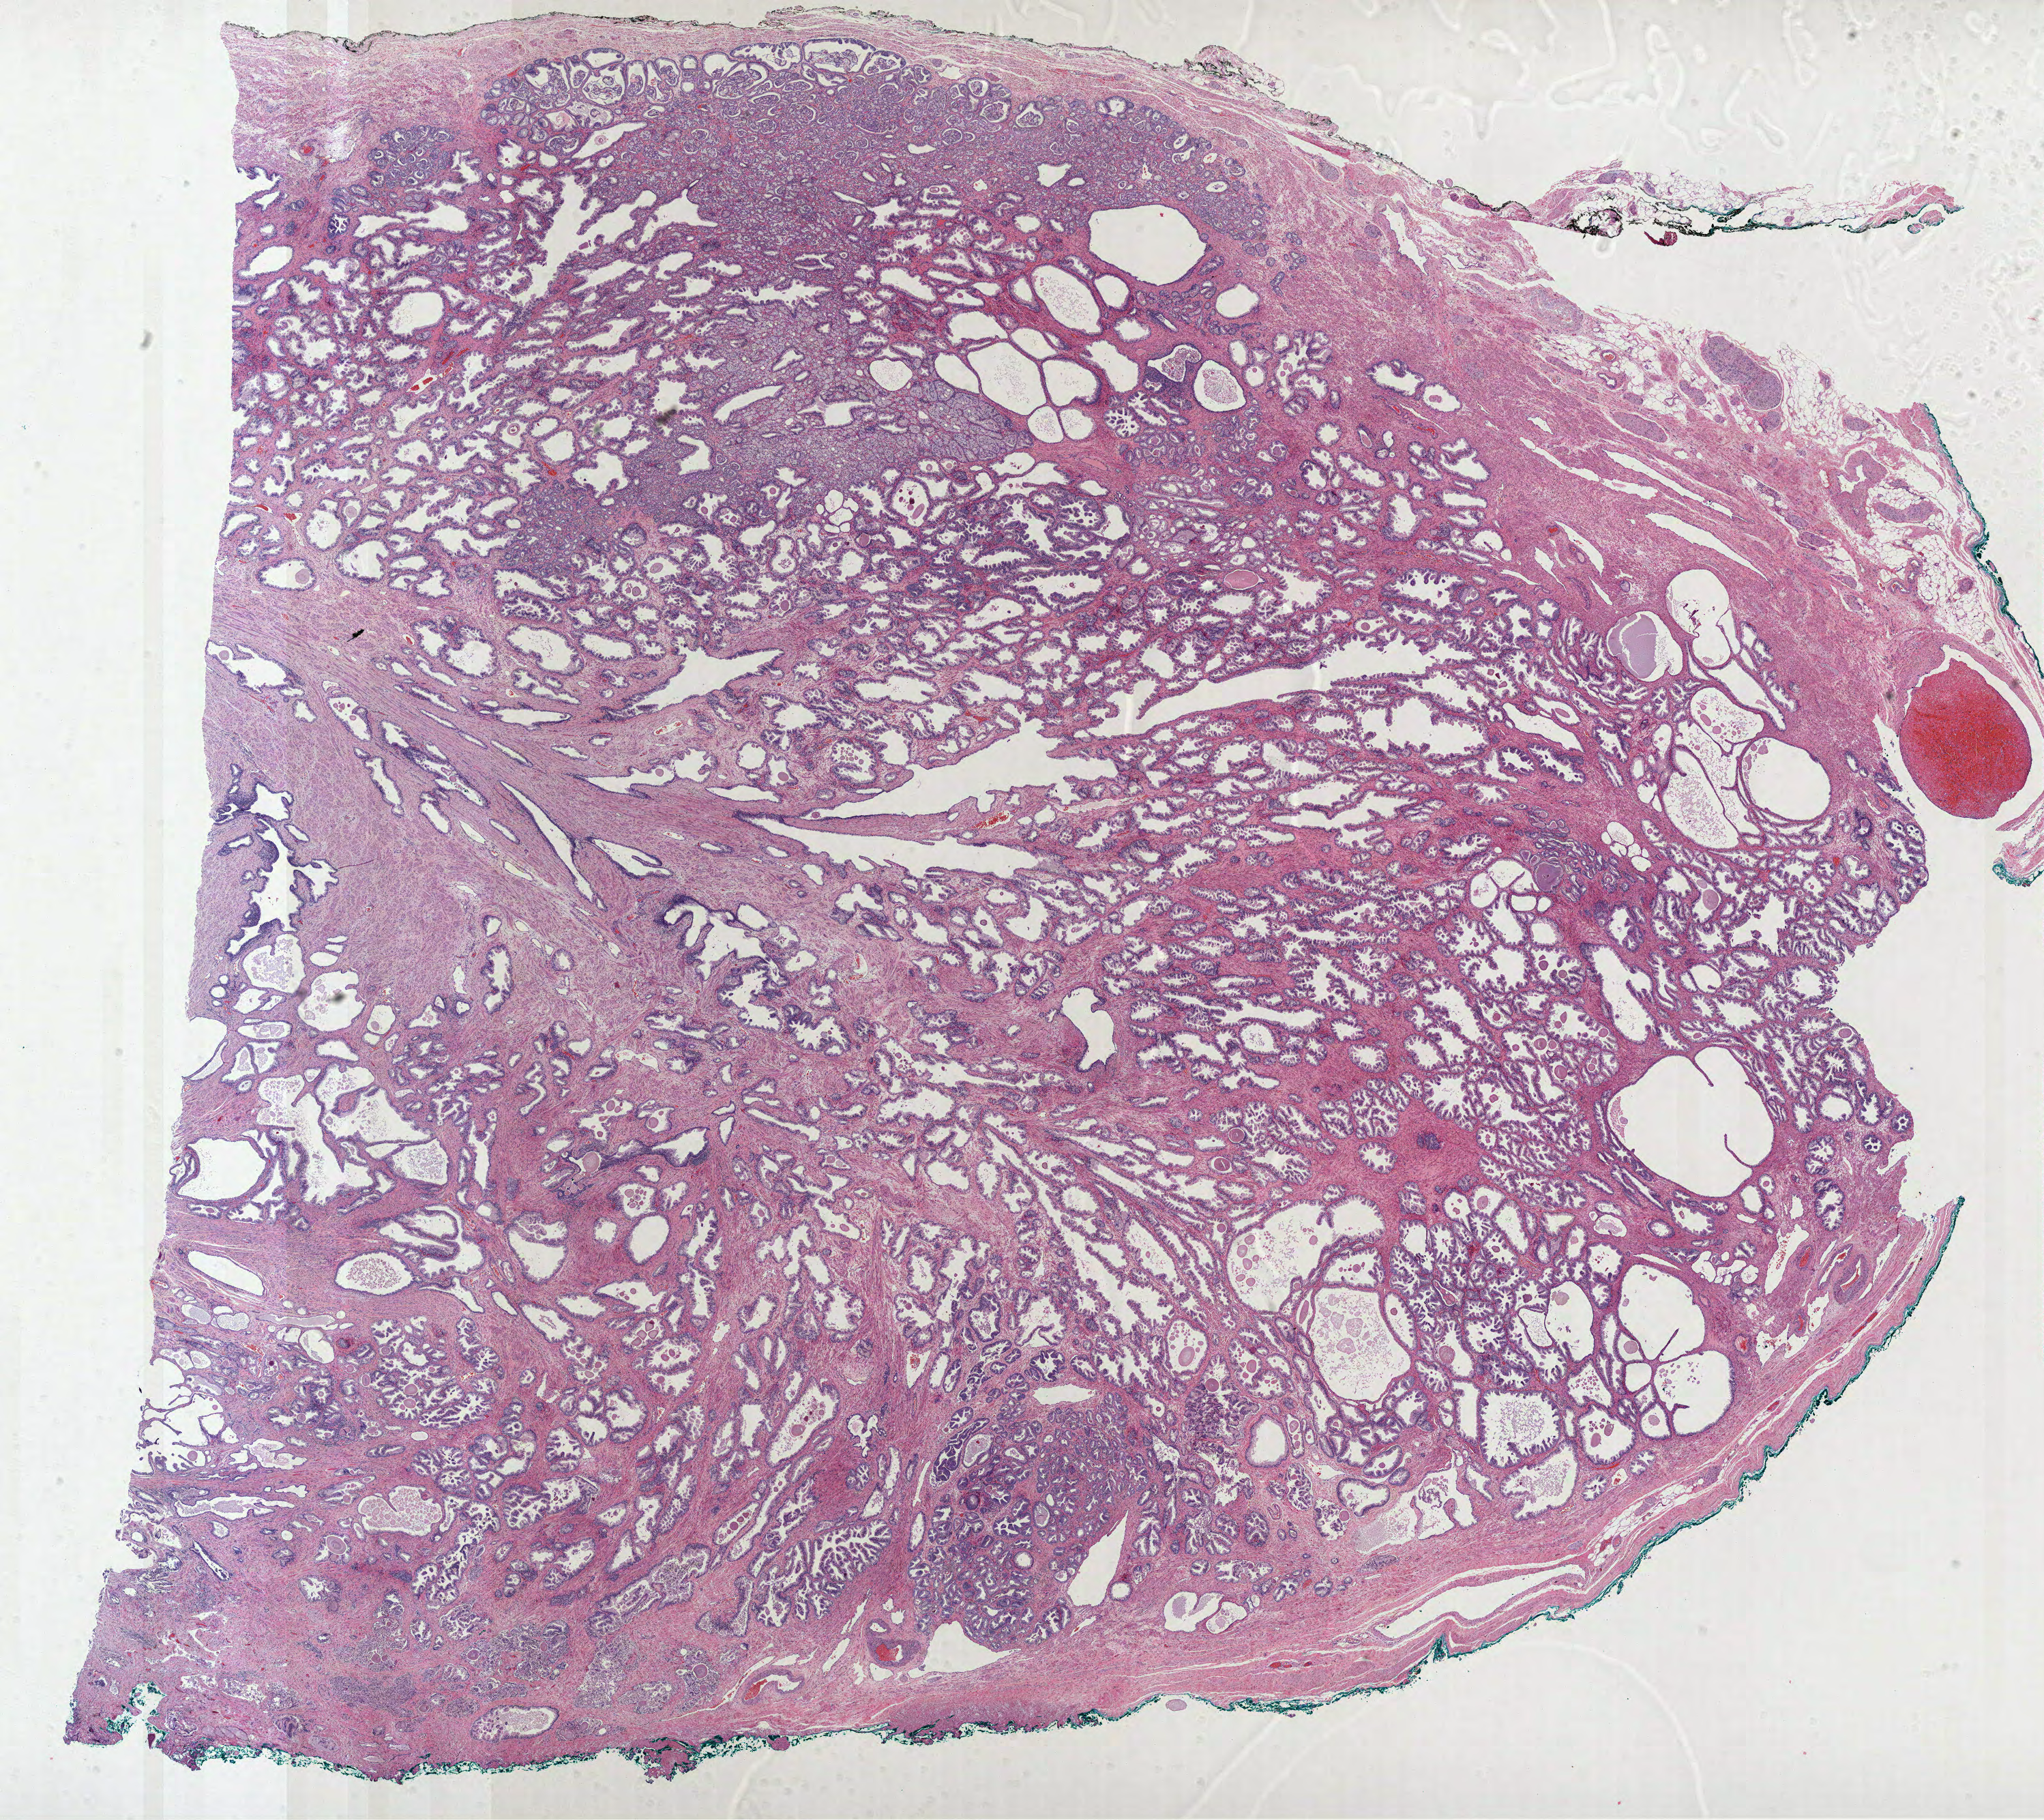
Whole-slide histology image, H&E, a low-resolution overview of the entire scanned area, about 24.2 x 21.5 mm (slide scanned at 40x). Formalin-fixed paraffin-embedded (FFPE) diagnostic section. Primary tumour sample from the prostate. Male, age 72 years at initial diagnosis. Gleason score: 7 (3+4).
• pathologic diagnosis: Acinar cell carcinoma
• laterality: bilateral